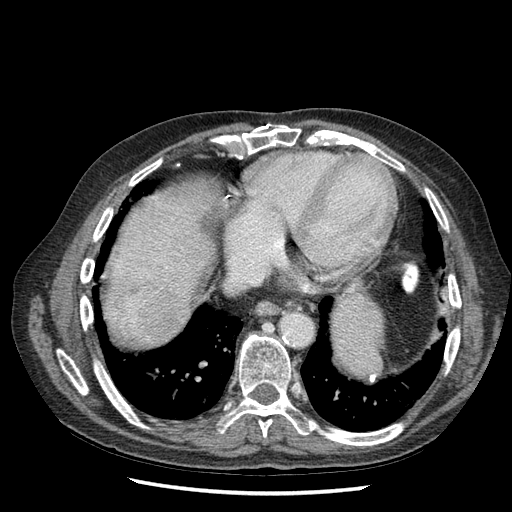
Contrast-enhanced abdominal CT (liver protocol), one axial slice; position 61 of 67 along the scan axis; reconstruction kernel STANDARD; 120 kVp; soft-tissue window (W 400 / L 40 HU); 2.5 mm slice thickness; 512 × 512 image matrix. From the clinical record (not read from this slice): diagnosis: hepatocellular carcinoma (patient treated with transarterial chemoembolisation; whether this scan precedes or follows treatment is not stated here); TNM stage (as recorded): Stage-I.
Annotated regions visible in this slice (semi-automatically segmented with operator editing):
- liver parenchyma outside the tumour (the mass and vessels are separate outlines, so this box may not span the whole liver): bounding box [x1, y1, x2, y2] px = [108, 182, 206, 316]
- mass: [118, 290, 178, 337]
- liver vessels: [167, 289, 170, 292]